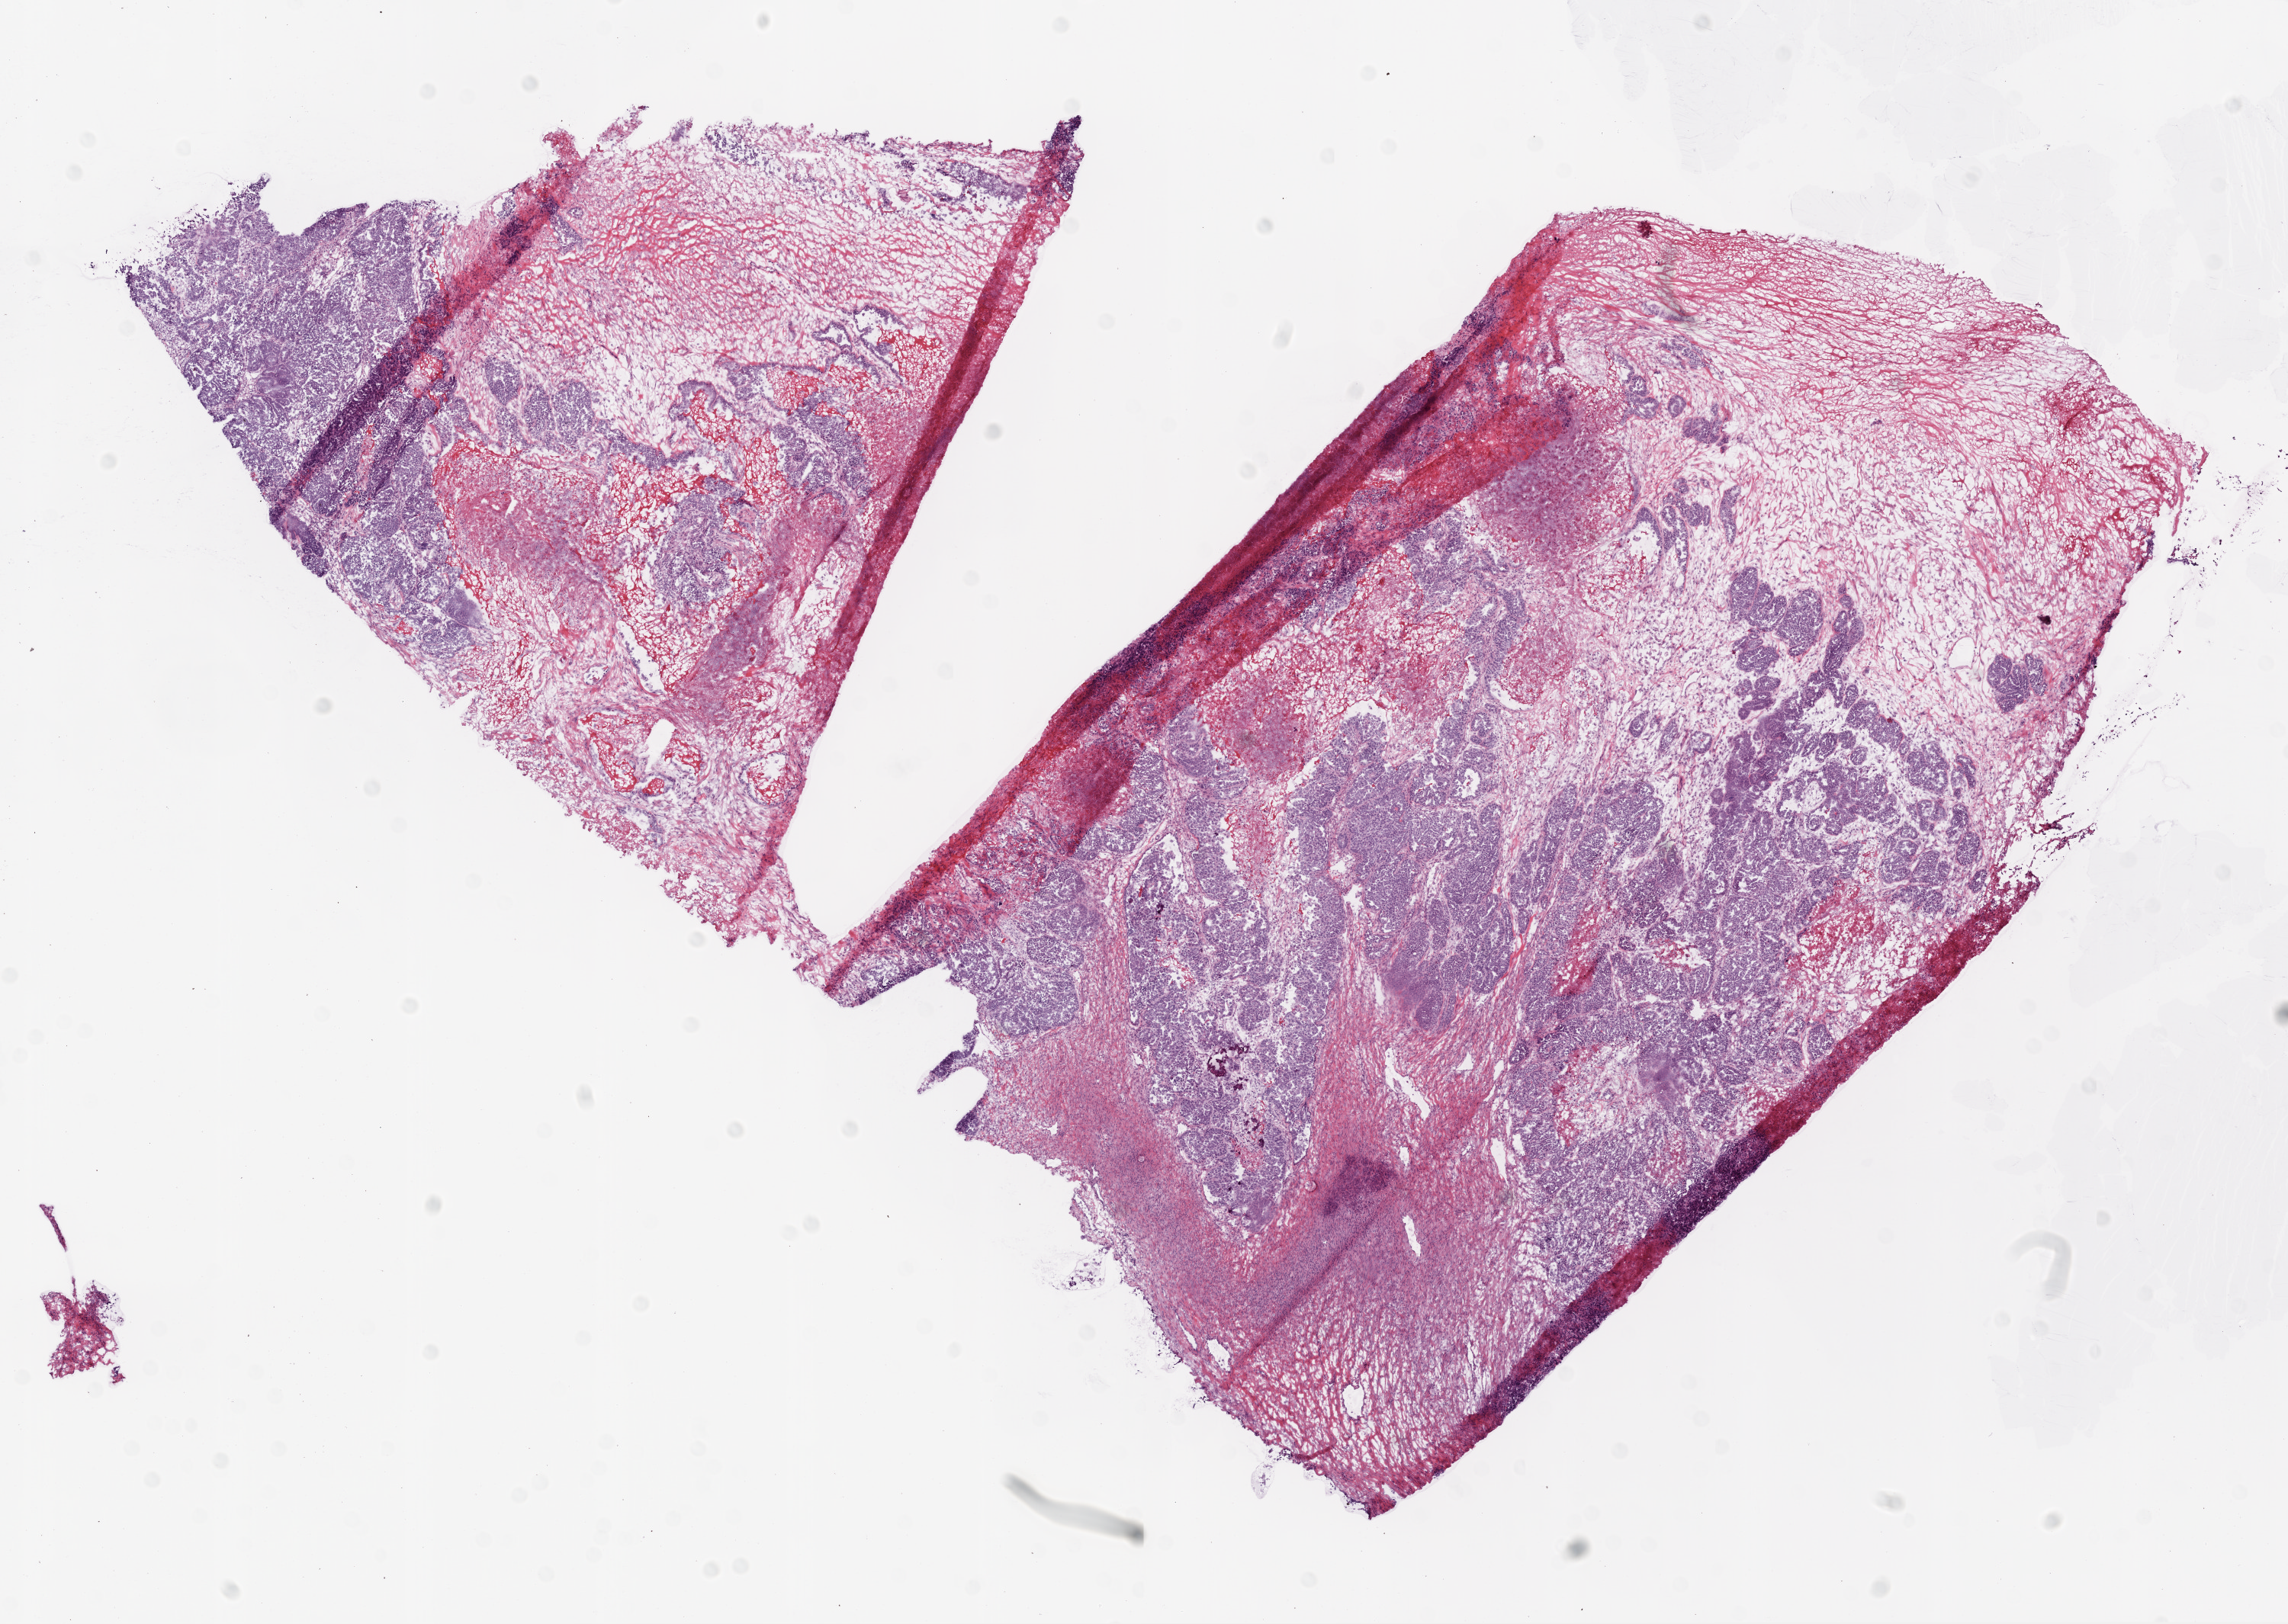
H&E-stained whole-slide image — whole scanned area (about 12.0 x 8.5 mm, acquisition: 20x scan) shown as a low-resolution overview. Frozen section from the top of the tissue portion. Sample: primary tumour, ovary. Patient: female, age at initial diagnosis 48 years. Histologic grade: G3 (poorly differentiated). Pathologist review of this section (percent, as recorded): tumour cells 30%, tumour nuclei 90%, normal cells 15%, stromal cells 40%, necrosis 15%.
Laterality: bilateral. FIGO stage: IIIC. Pathologic diagnosis: Serous cystadenocarcinoma, NOS.